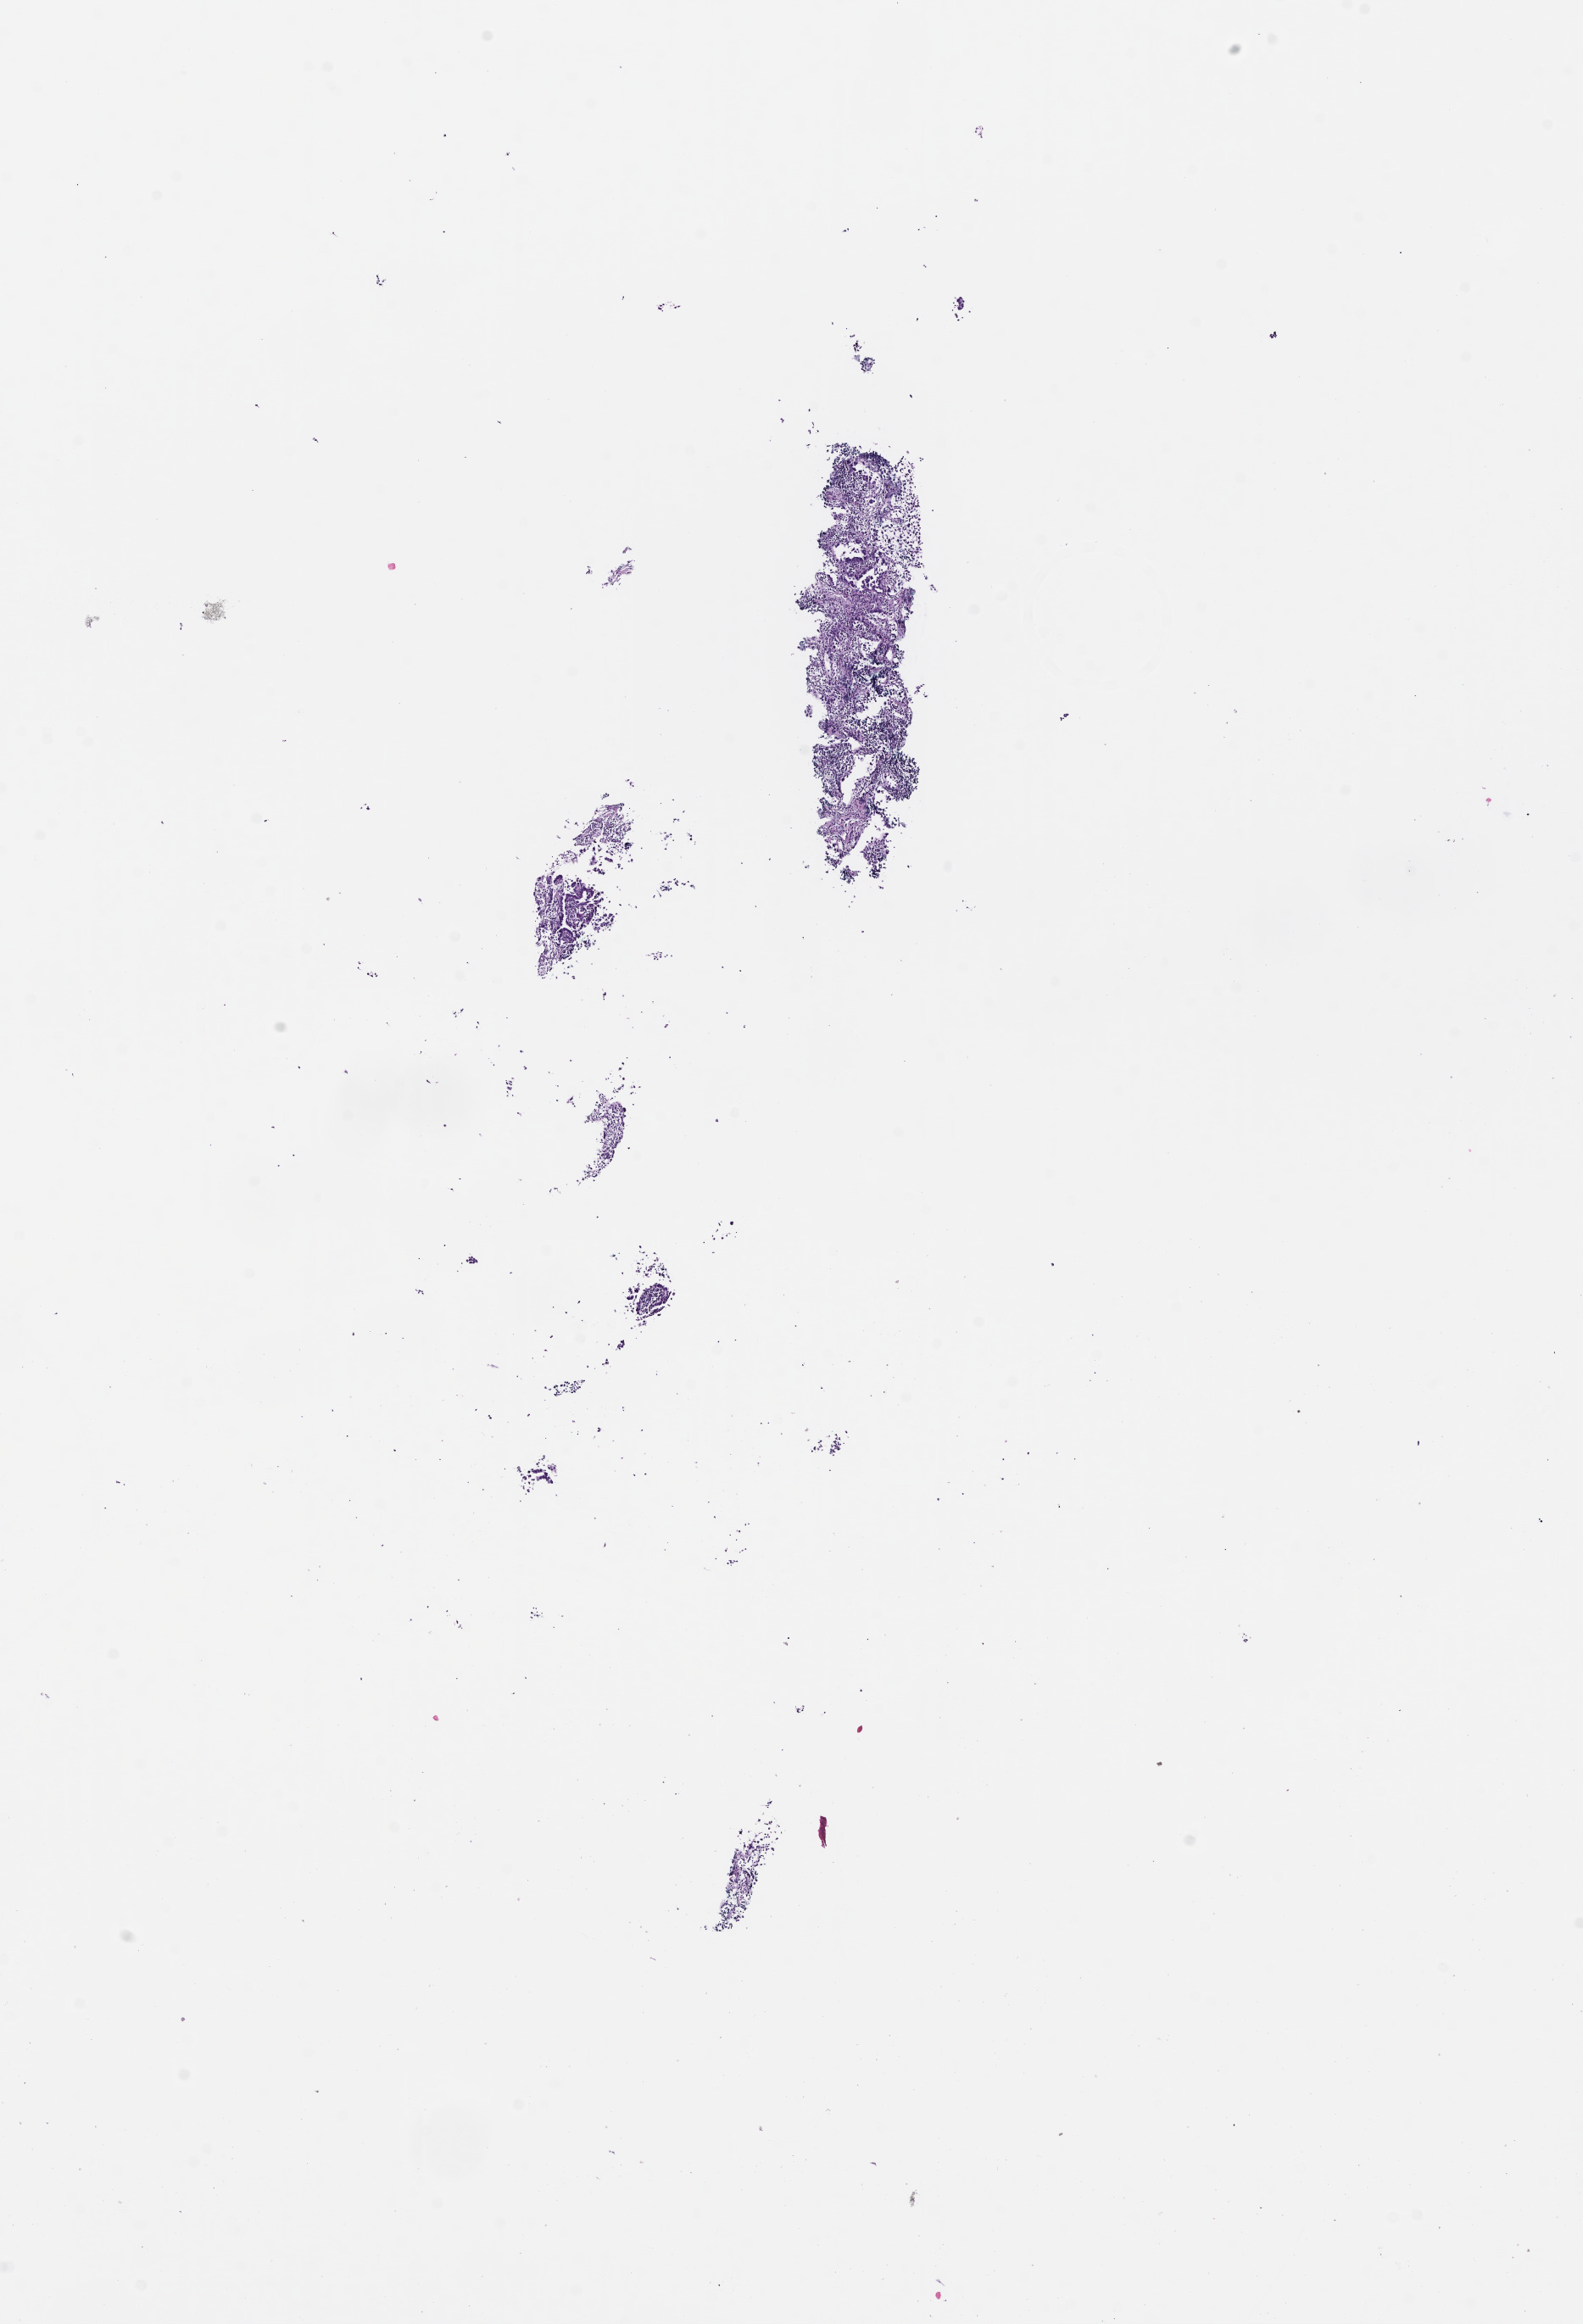
Digitized hematoxylin and eosin (H&E)-stained section — whole scanned area (about 7.5 x 11.1 mm) shown as a low-resolution overview, formalin-fixed, paraffin-embedded (FFPE) tissue, tissue site: lung. Female patient.
* this section: primary tumour tissue
* diagnosis: Non-Small Cell Lung Carcinoma